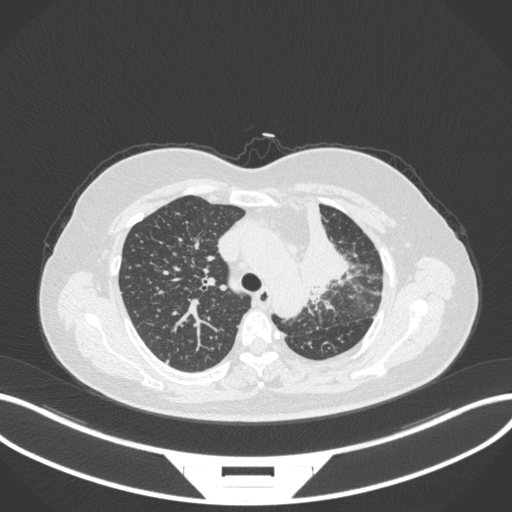
Chest CT, one axial slice. Slice 243 of 348 in the series (ordered by position). Reconstruction kernel B31f. 120 kVp. Lung window (W 1500 / L -600 HU). 1 mm slice thickness. 512 × 512 image matrix, field of view 400 × 400 mm. Patient: female, 49 years. From the clinical record (not read from this slice): clinical TNM (as recorded): T1c N0 M1.
Outlined on this slice (rectangle marked by the reading radiologist):
- lung tumour (recorded histology: adenocarcinoma): bounding box <294,196,351,299> (left, top, right, bottom; pixels)